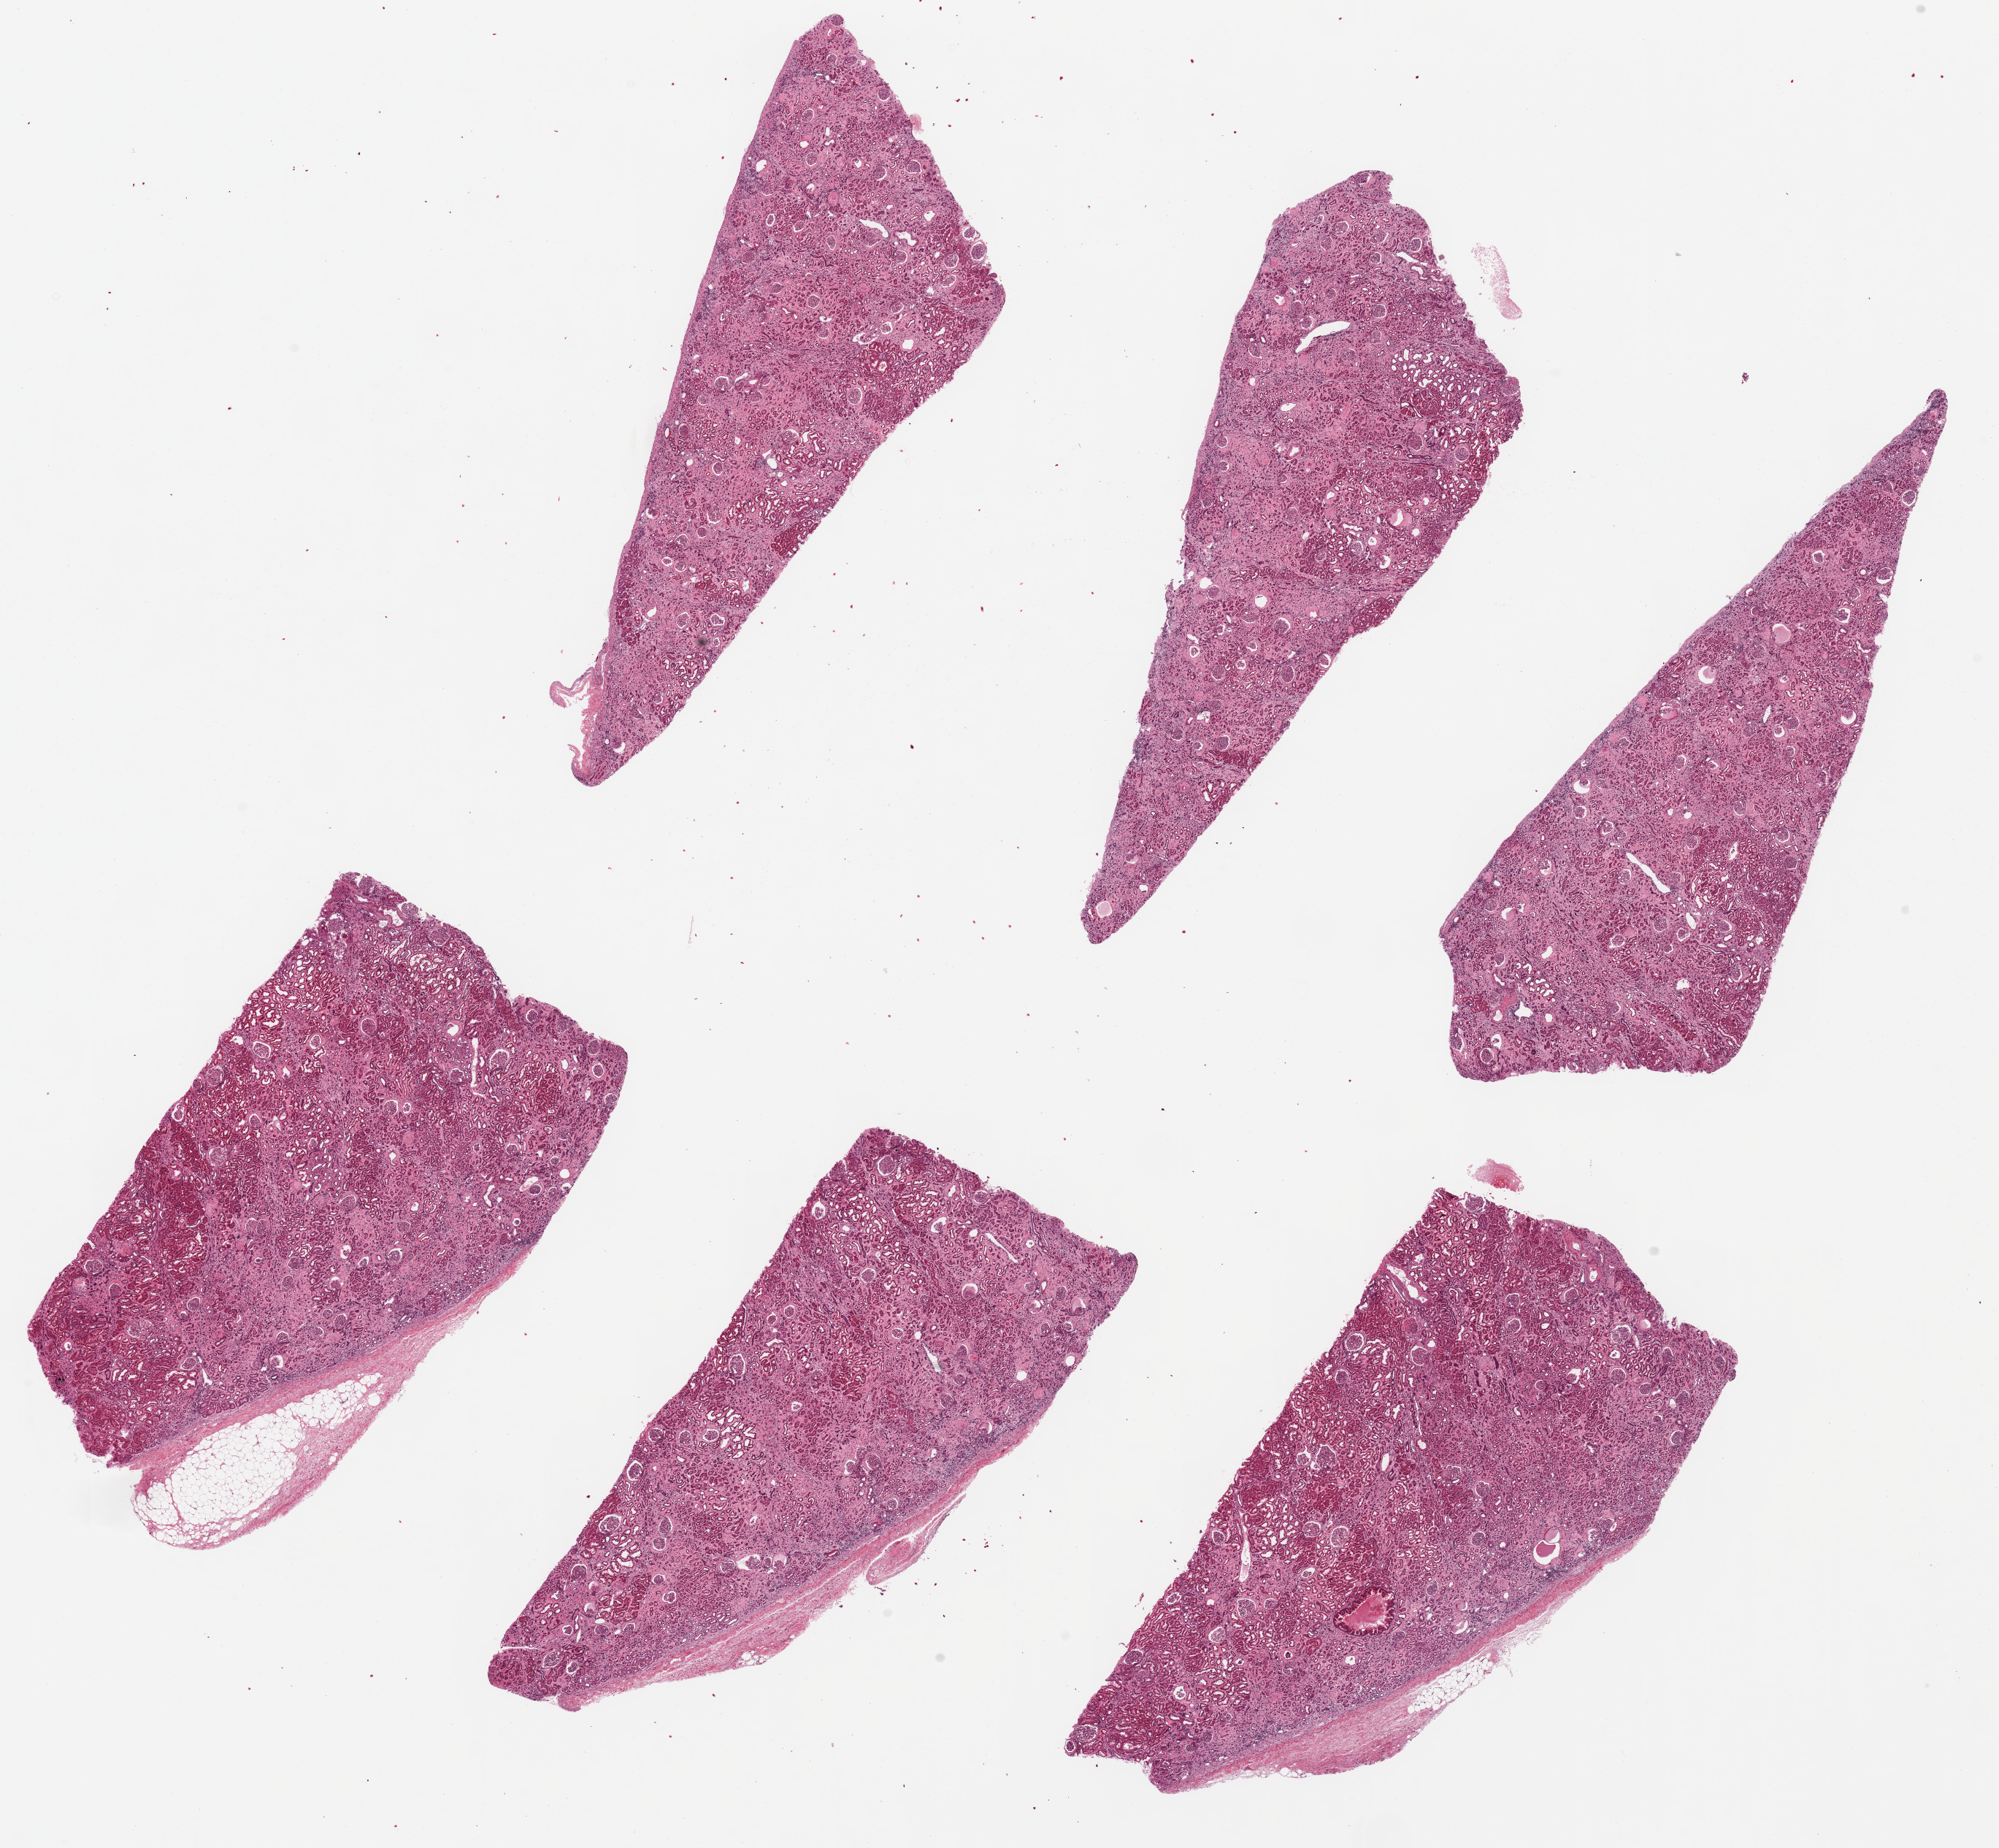
Hematoxylin and eosin (H&E) whole-slide image — a low-resolution overview of the entire scanned area, about 21.7 x 20.0 mm. PAXgene-fixed paraffin-embedded (PFPE) section. Target tissue: renal cortex. Tissue donor sample. Donor sex: male.
Pathologist's review note for this sample: 6 ~8.5x3.5mm pieces. Diffuse interstitial fibrosis with chronic interstitial nephritis.